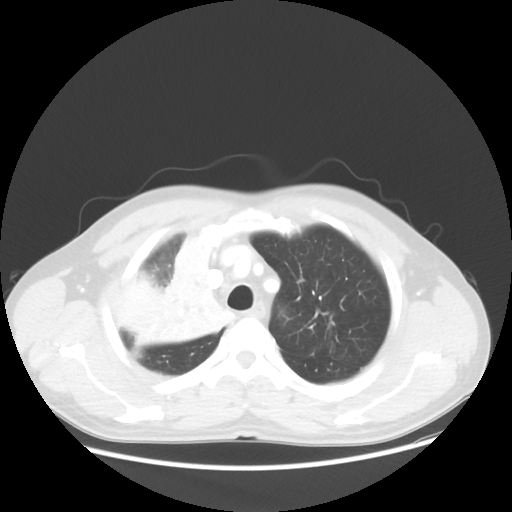
Chest CT, one axial slice; position 43 of 56 along the scan axis; reconstruction kernel STANDARD; lung window (W 1500 / L -600 HU); 5 mm slice thickness; 512 × 512 image matrix. Patient: male, 60 years. From the clinical record (not read from this slice): clinical TNM (as recorded): T2a N1 M0.
Outlined on this slice (bounding box drawn by a radiologist):
- lung tumour (recorded histology: squamous cell carcinoma): bounding box [x1, y1, x2, y2] px = [125, 236, 234, 358]